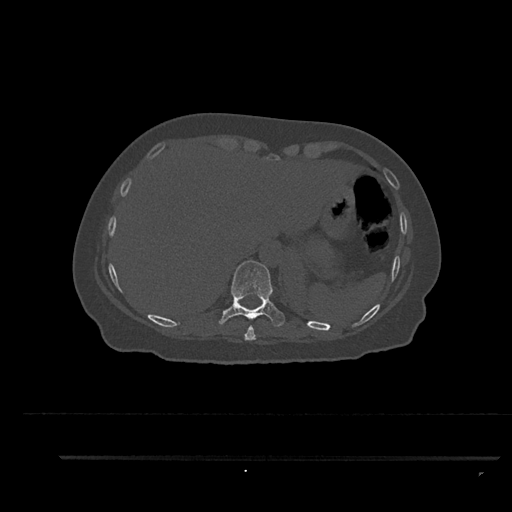
CT including the spine, one axial slice. Slice 369 of 797 in the series (ordered by position). Bone window (W 1800 / L 400 HU). 0.5 mm slice thickness. 512 × 512 image matrix. Female patient, age 44 years. Case-level facts recorded for this patient, not image findings: primary cancer: renal.
Structures marked on this image (semi-automatically segmented with operator editing):
- T10 vertebra: bounding box [x1, y1, x2, y2] px = [218, 260, 285, 330]
- T9 vertebra: [244, 326, 256, 340]